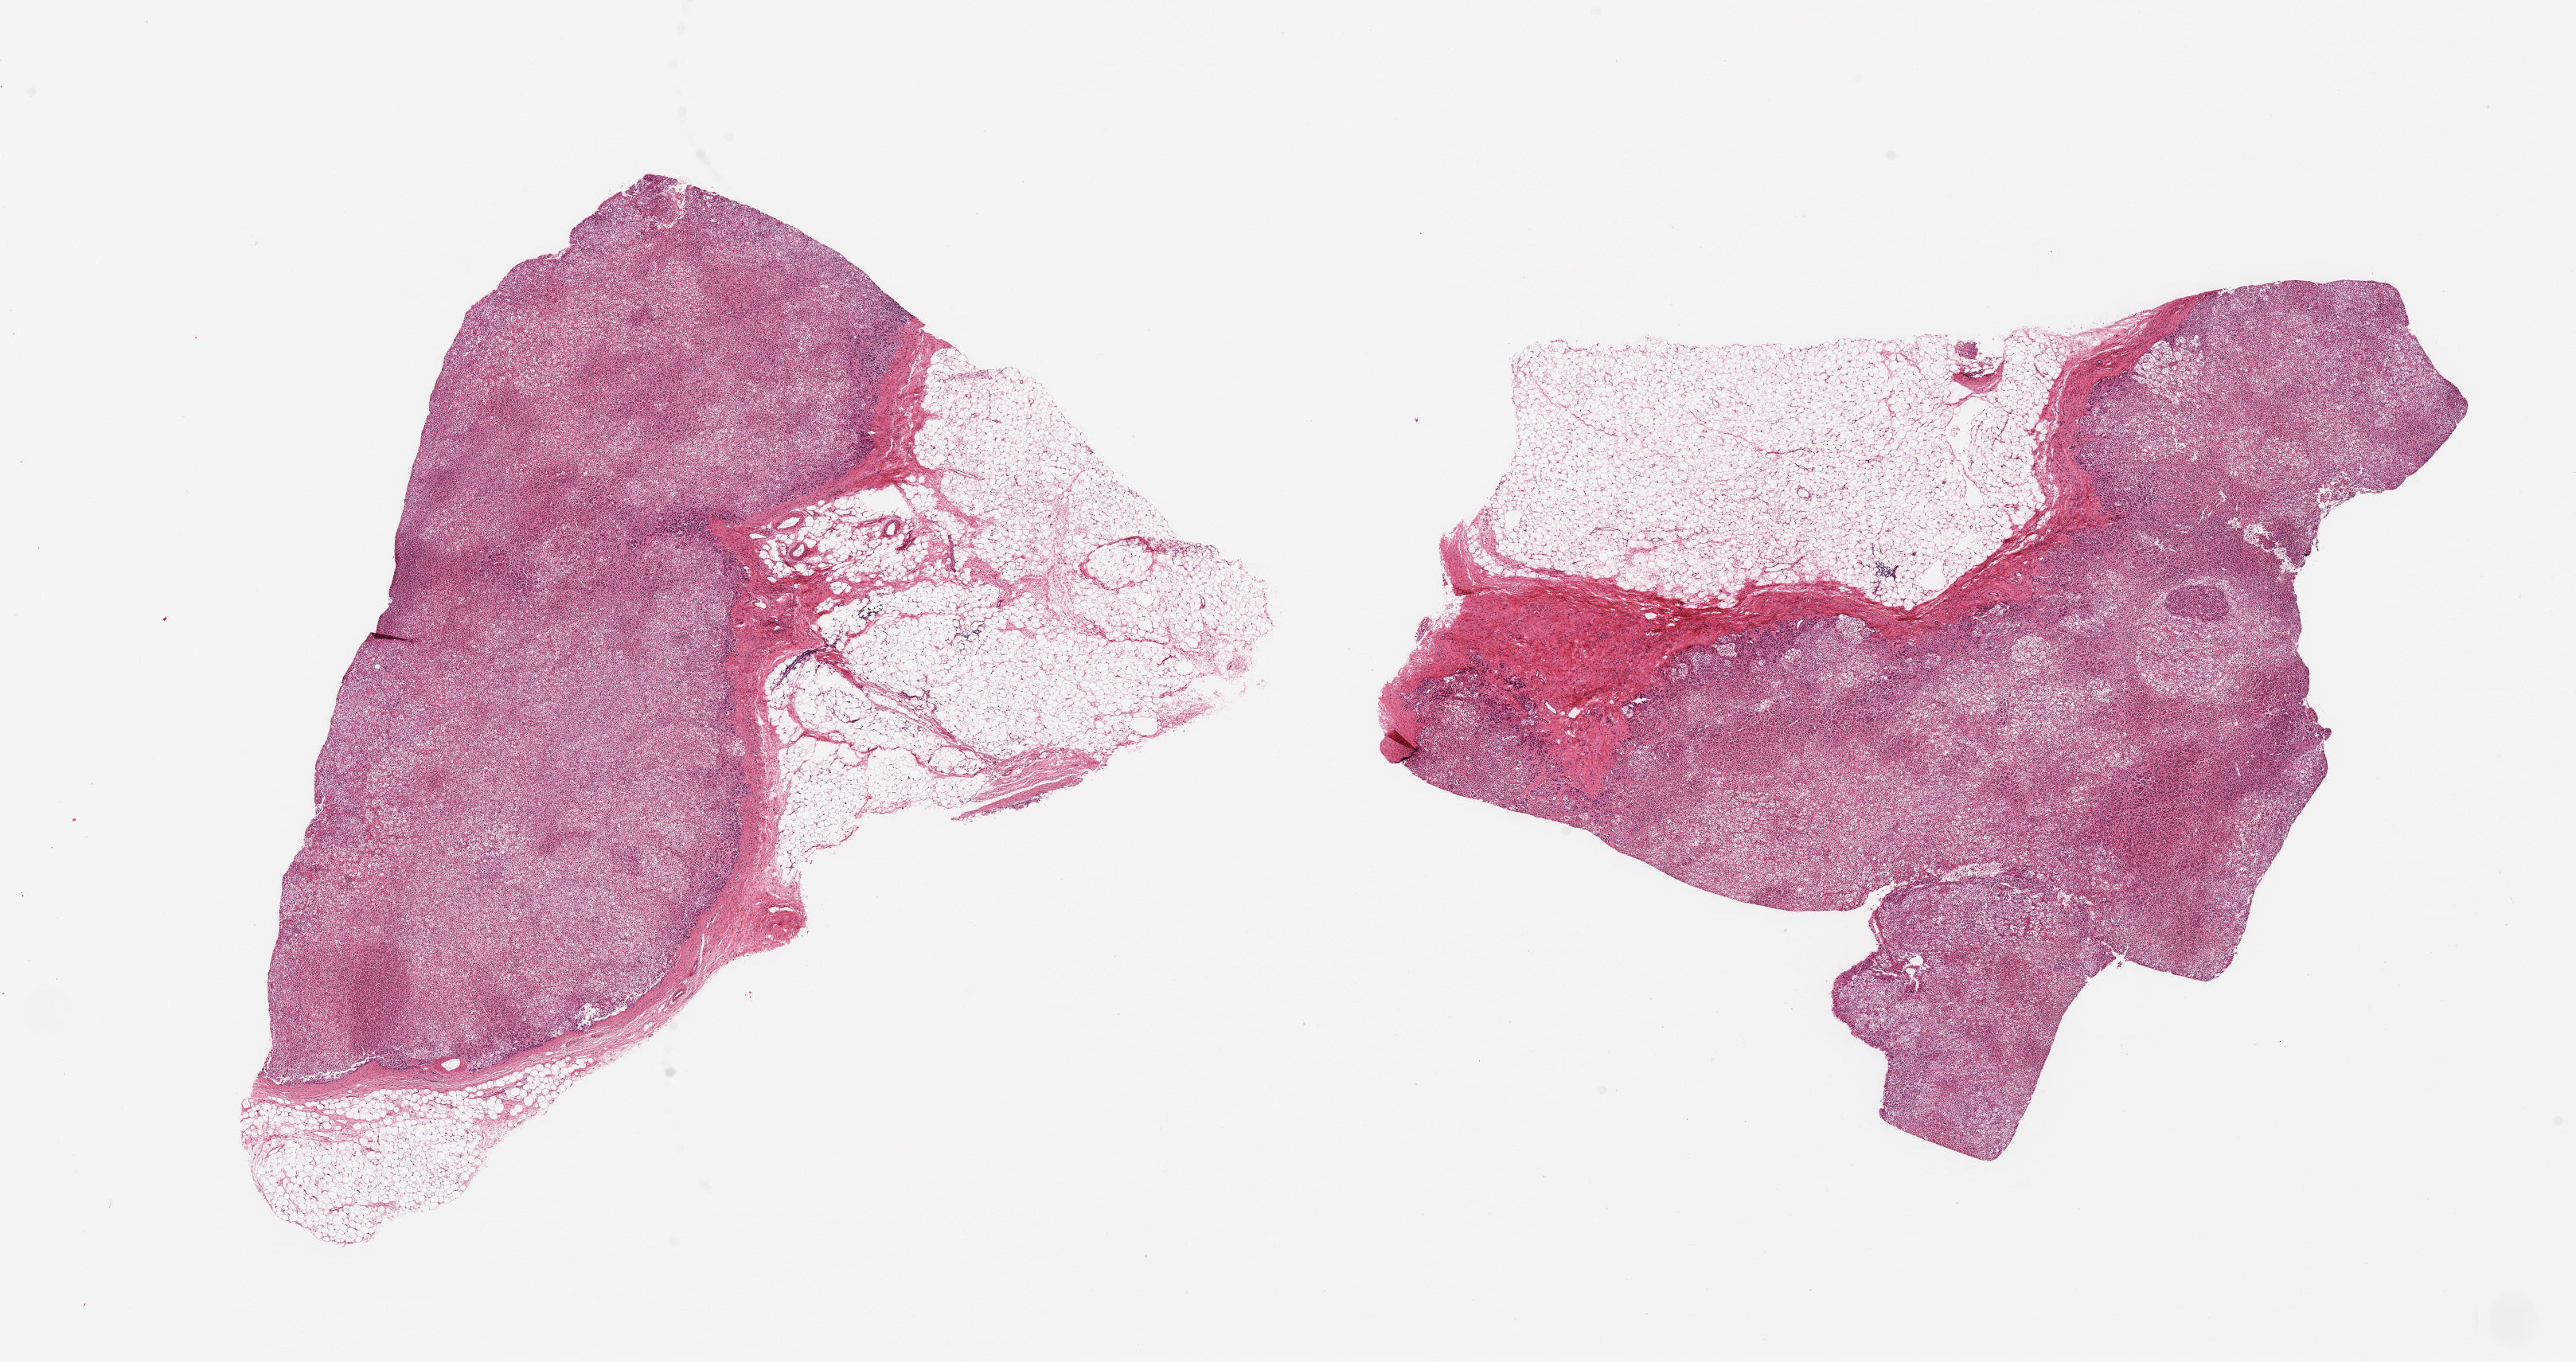
Hematoxylin and eosin (H&E) whole-slide image, brightfield — a low-resolution overview of the entire scanned area, about 25.6 x 13.5 mm, PAXgene-fixed paraffin-embedded (PFPE) section, sampled site (target tissue): adrenal gland, tissue donor sample. Donor: male.
Reviewer comment on this tissue sample: 2 pieces; 40% external adipose content.